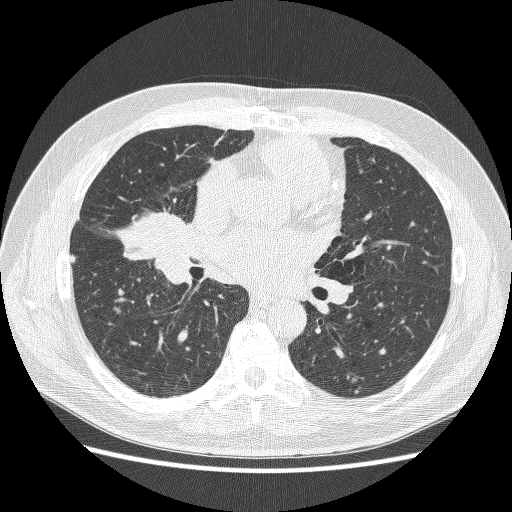
Axial slice from a low-dose chest CT screening exam, baseline annual screen, lung window (W 1500 / L -600 HU), 1.25 mm slice thickness. Male, age 59 years at enrolment. Former smoker at enrolment.
• Expert reader's lesion annotation, bounding box (x1, y1, x2, y2) in pixels: (123, 194, 197, 265).
• Screening reader's record for this exam: no non-calcified nodule ≥4 mm recorded.
• Lung cancer was diagnosed 24 days after this screen: adenocarcinoma, NOS, right middle lobe, poorly differentiated (G3), stage IV (AJCC 6th edition), 54 mm at pathology.